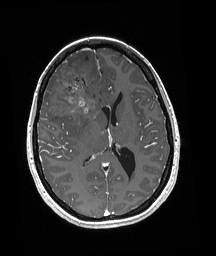
Brain MRI from a brain-tumour surgery series, one axial slice; slice 89 of 192 in the series (ordered by position); T1-weighted post-contrast; 1 mm slice thickness; 216 × 256 image matrix. From the clinical record (not read from this slice): histopathology: Oligodendroglioma; WHO grade: 3; IDH mutation: yes.
Annotated regions visible in this slice (expert manual segmentation):
- tumour: bounding box <52,64,103,117> (left, top, right, bottom; pixels)